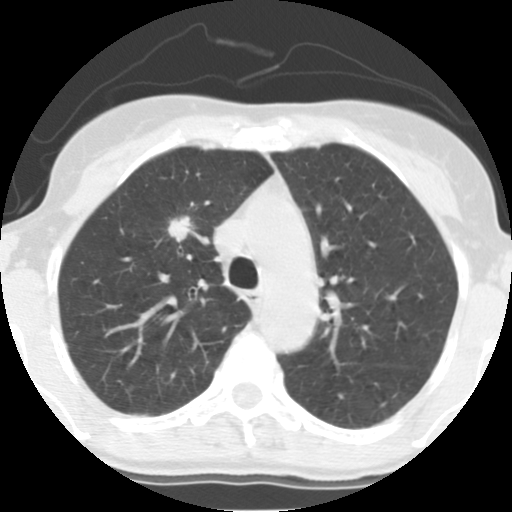
Low-dose screening chest CT, axial slice, third annual screen, lung window (W 1500 / L -600 HU), standard (soft-tissue) reconstruction kernel (STANDARD), 140 kVp, 512 × 512 image matrix. Female, age 56 years at enrolment.
Expert reader's lesion annotation, bounding box [x1, y1, x2, y2] px = [160, 209, 201, 251]. Reader record for this screening exam (exam-level; its link to the box is not recorded): non-calcified nodule or mass ≥4 mm, right upper lobe, 17 × 12 mm, spiculated (stellate) margins, soft tissue attenuation, pre-existing on the prior screen: yes; interval growth: yes. Official screen result: positive, other.